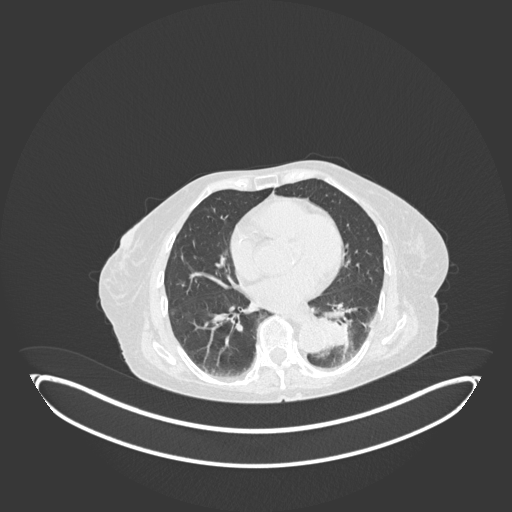
Chest CT, one axial slice; slice 46 of 189 in the series (ordered by position); reconstruction kernel B30f; 120 kVp; lung window (W 1500 / L -600 HU); 1 mm slice thickness; 512 × 512 image matrix, field of view 500 × 500 mm. Female patient, age 82 years. From the clinical record (not read from this slice): clinical TNM (as recorded): T1b N0 M1.
Annotated regions visible in this slice (bounding box drawn by a radiologist):
- lung tumour (recorded histology: adenocarcinoma): bounding box [x1, y1, x2, y2] px = [315, 315, 353, 352]